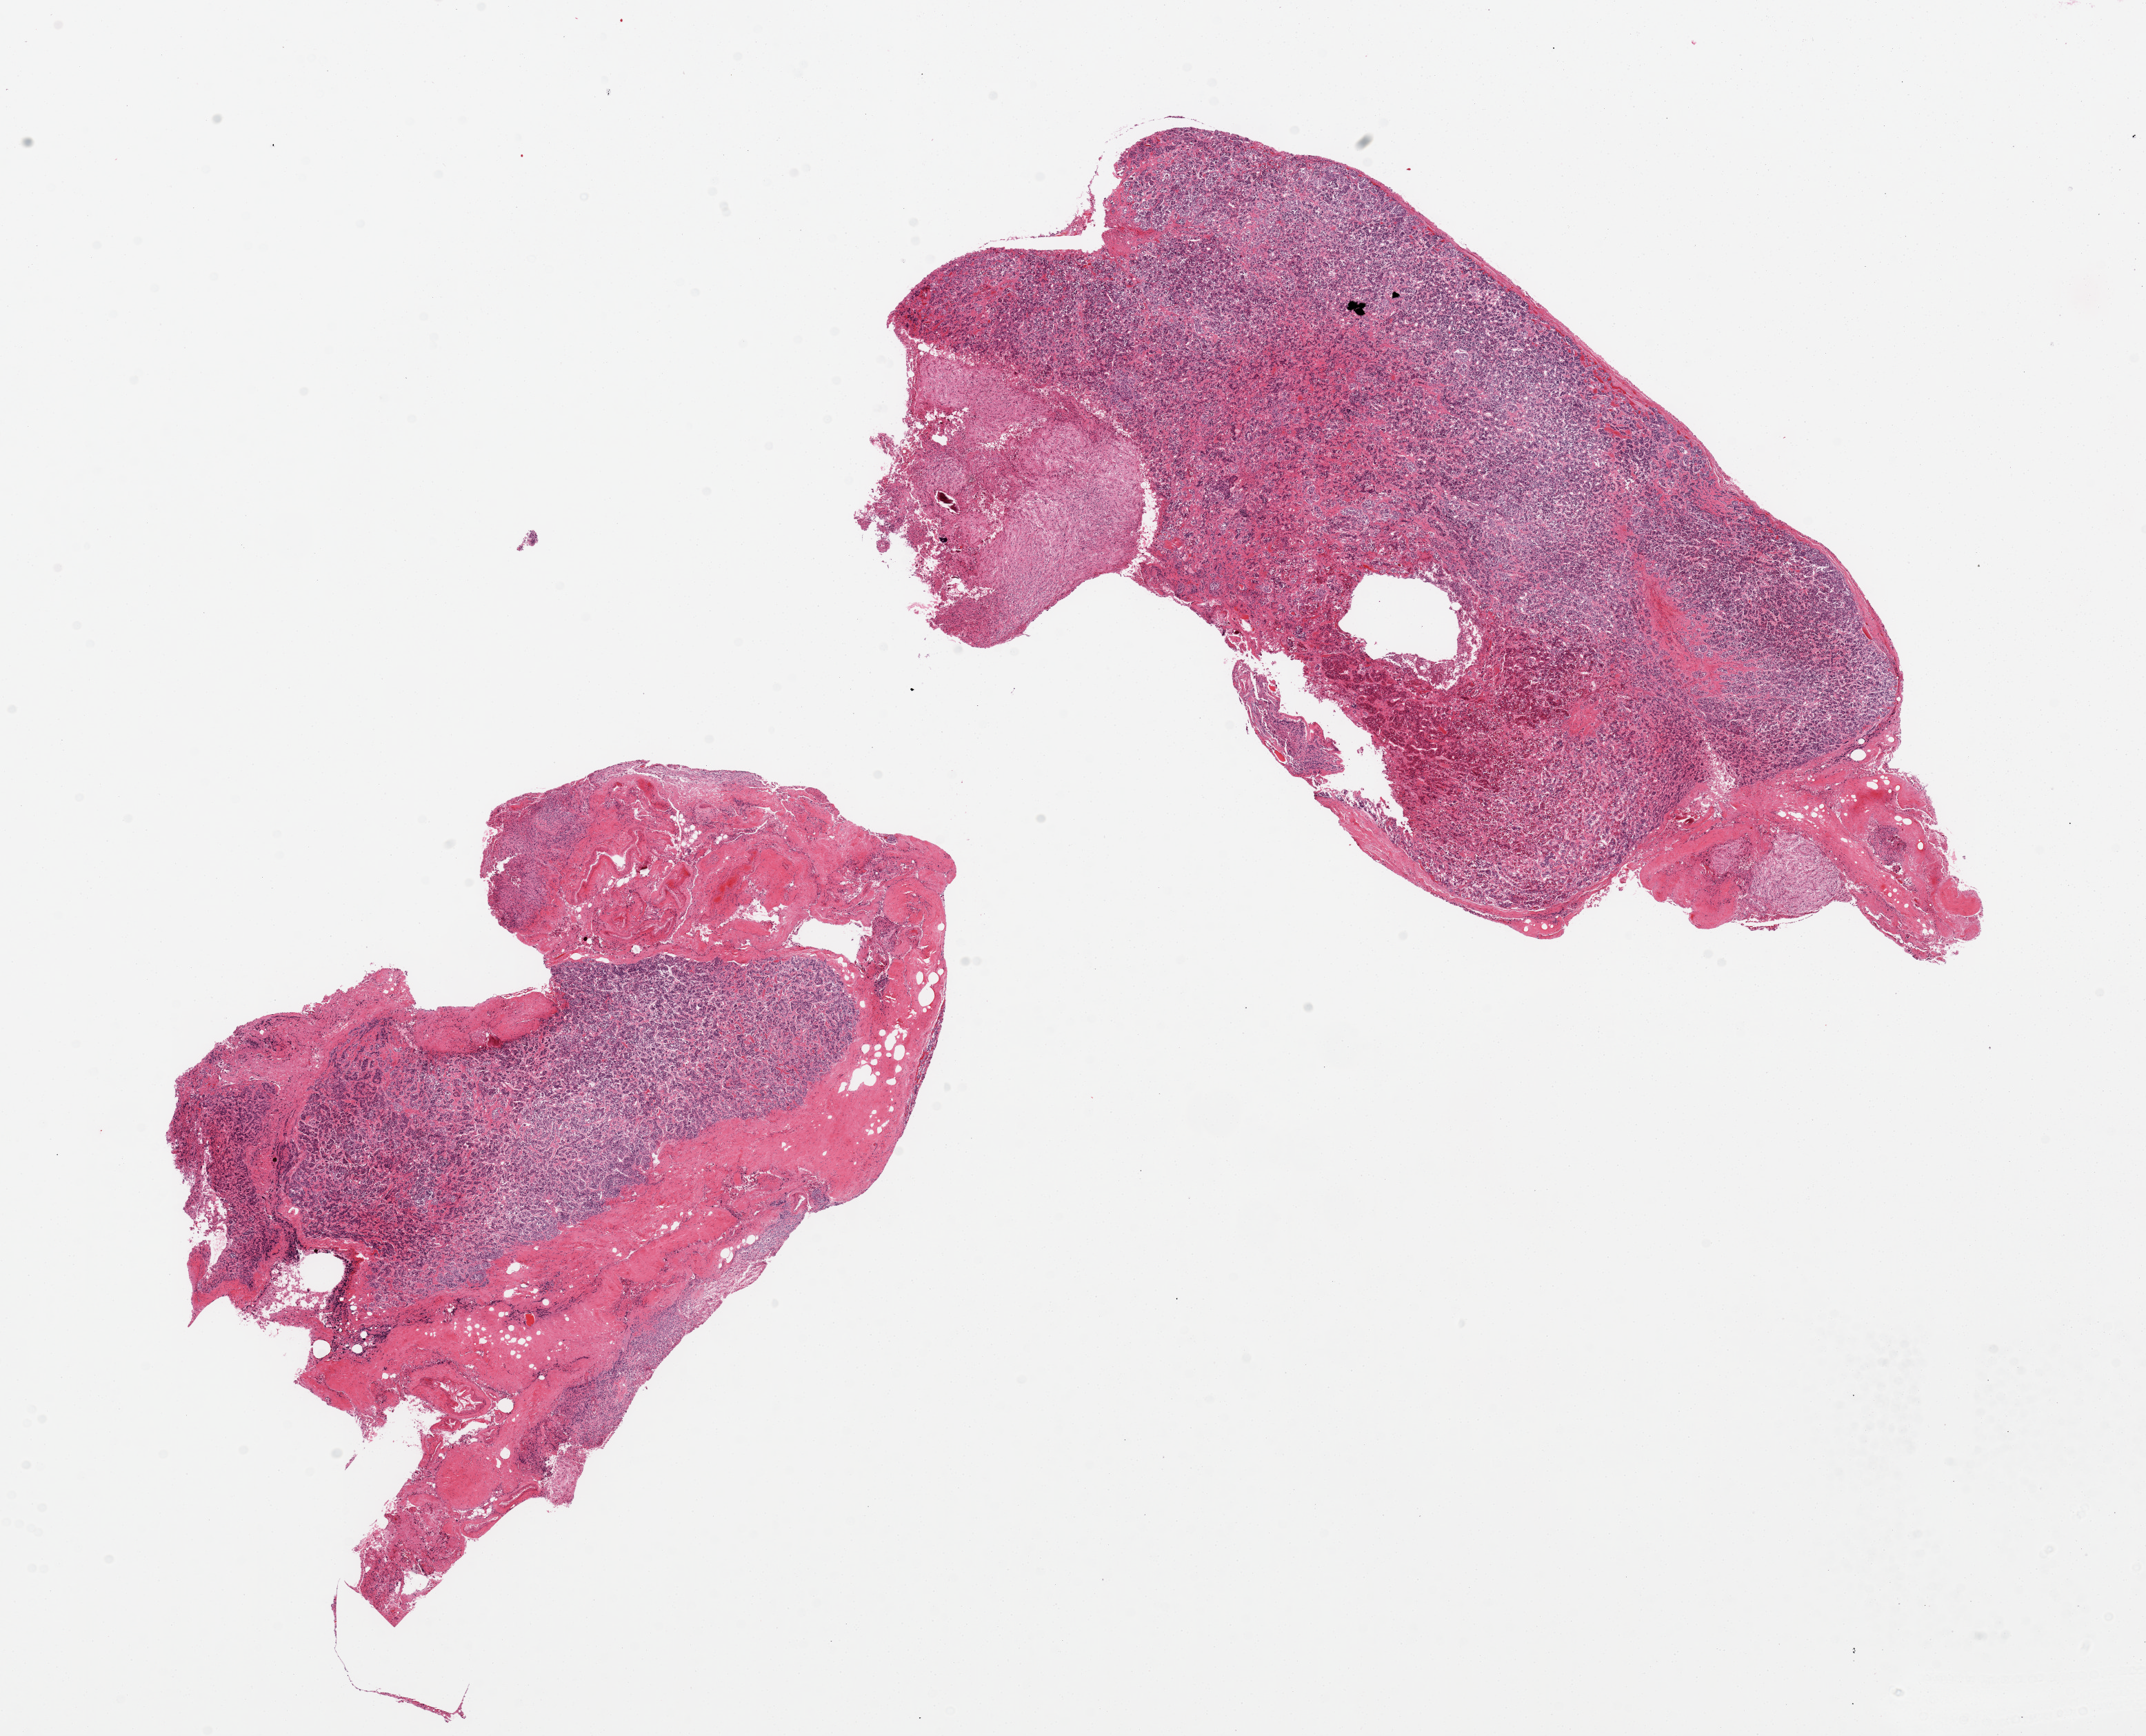
Digitized H&E-stained section, whole scanned area (about 24.6 x 19.9 mm) shown as a low-resolution overview, PAXgene-fixed, paraffin-embedded tissue, sampled site (target tissue): pituitary, donor tissue sample. Donor sex: male.
Review note (as recorded): 2 pieces, adenophypophysis and neurohypophysis.